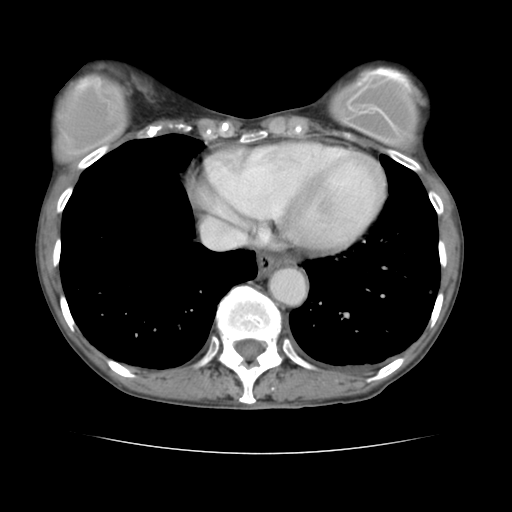
Contrast-enhanced abdominal CT, one axial slice. 120 kVp. Intravenous contrast given. Soft-tissue window (W 400 / L 40 HU). 2.5 mm slice thickness. 512 × 512 image matrix, field of view 319 × 319 mm. Female patient, age 77 years. Case-level facts recorded for this patient, not image findings: diagnosis: colorectal cancer liver metastases, imaged before liver resection; multiple liver metastases: yes; largest metastasis: 3 cm; disease in both lobes: no.
Outlined on this slice (expert manual segmentation):
- hepatic veins: bounding box <215,236,245,245> (left, top, right, bottom; pixels)